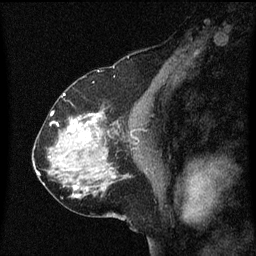
Breast MRI (dynamic contrast-enhanced), one sagittal slice; dynamic contrast-enhanced series, image 2 of 3 at this slice position (ordered by acquisition); 1.5 T; TE 4.2 ms, TR 8.4 ms; 2 mm slice thickness; 256 × 256 image matrix, field of view 200 × 200 mm. Patient: female, 58 years.
Outlined on this slice (semi-automatic segmentation, software-assisted and operator-edited):
- analysis volume of interest (the breast-tissue region the enhancement analysis was run in; not a lesion): bounding box <58,114,99,151> (left, top, right, bottom; pixels)
- tumour enhancement mask (voxels above the 70 % enhancement threshold inside the analysis volume of interest): <68,114,97,139>